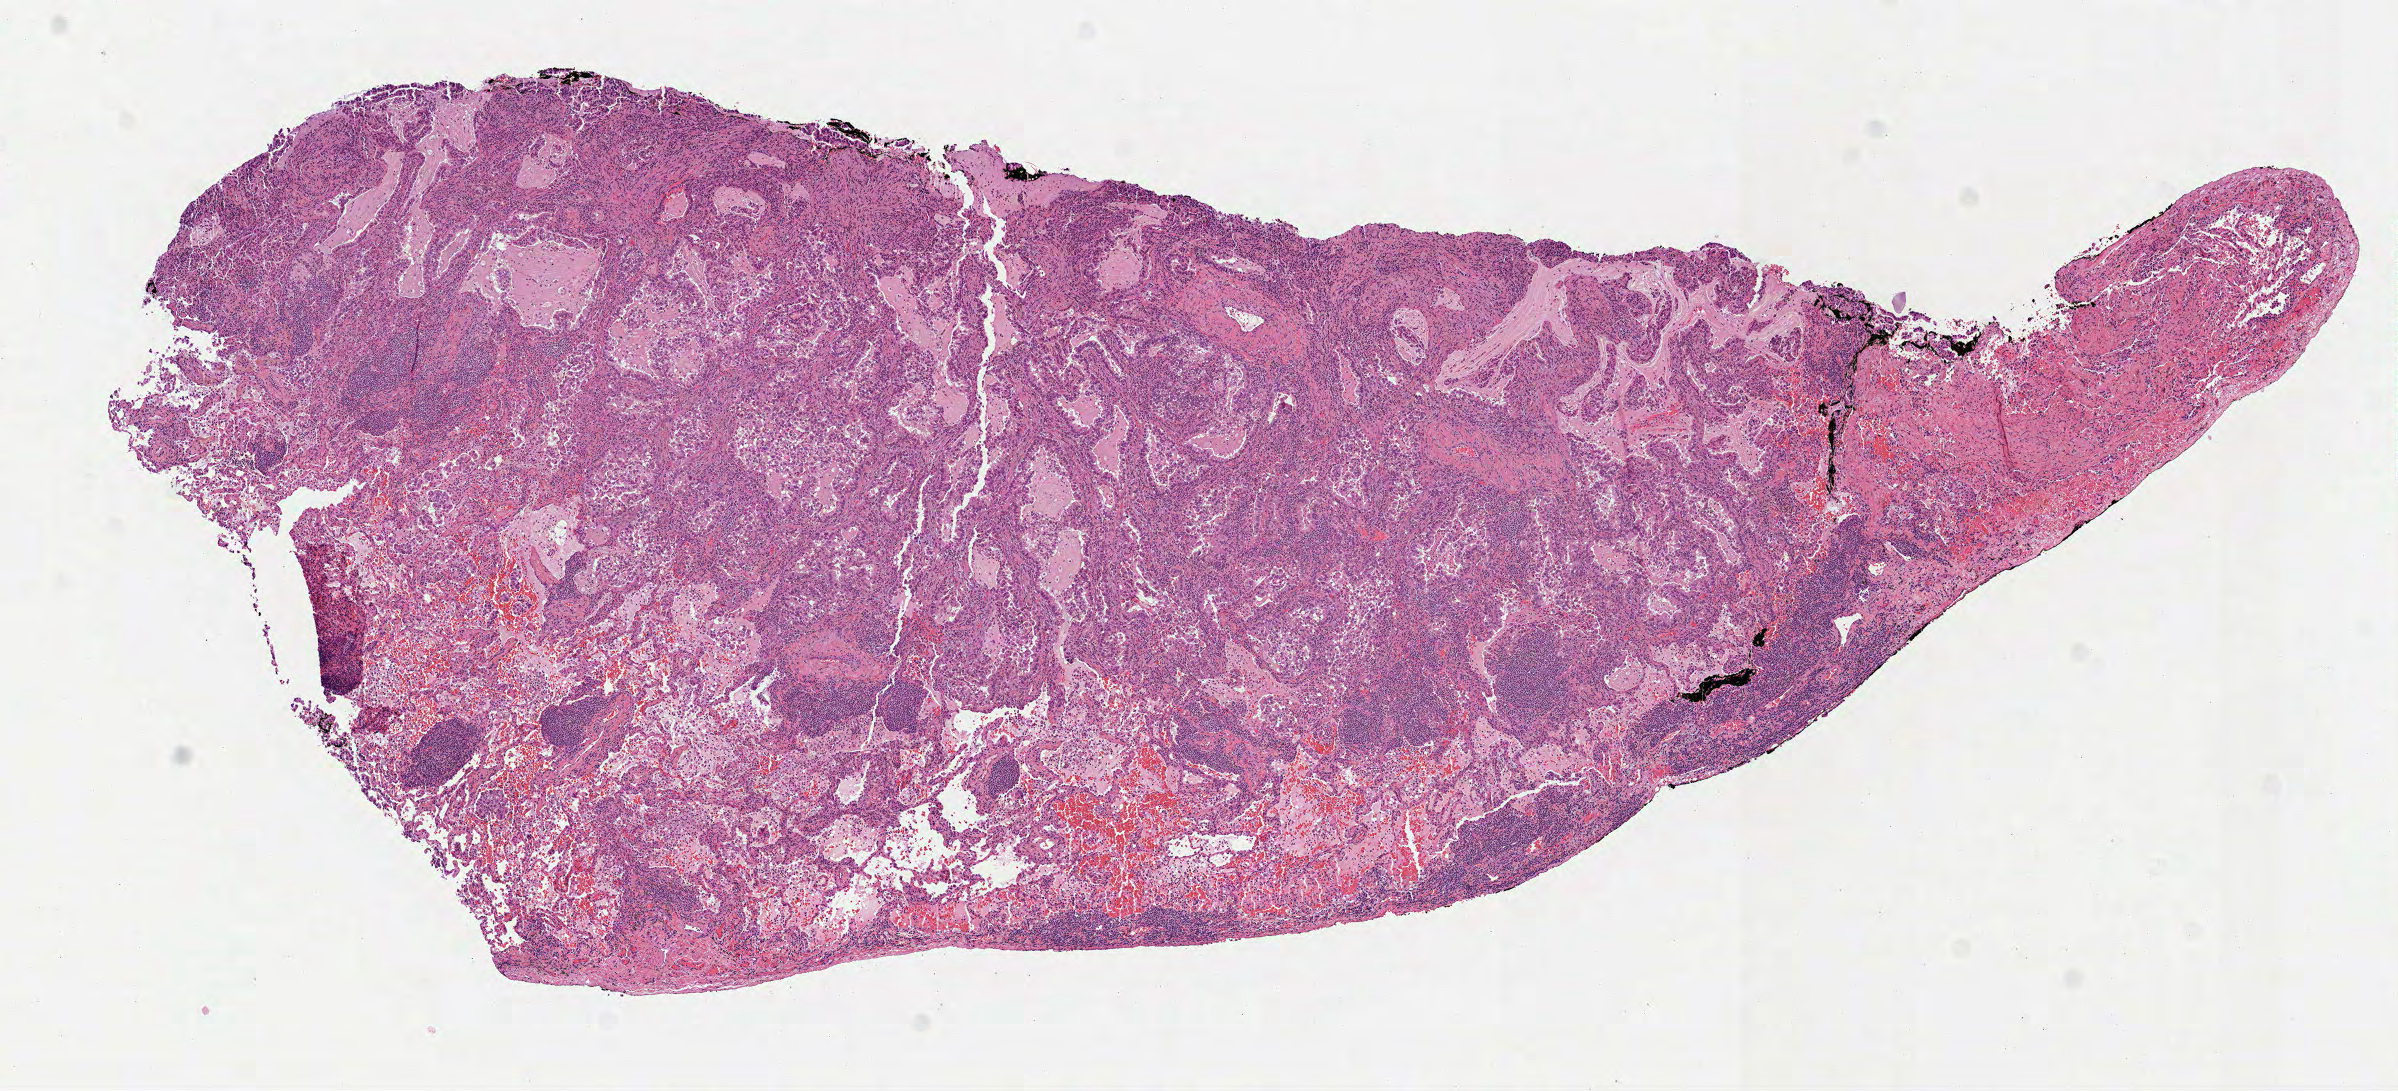
H&E-stained whole-slide image — a low-resolution overview of the entire scanned area, about 9.7 x 4.4 mm (slide scanned at 40x), FFPE section, sample: primary tumour, lung. Female, age 69 years at initial diagnosis.
Diagnosis: Adenocarcinoma, NOS (lower lobe, lung). Laterality: right. AJCC pathologic stage: IA. TNM: T1b N0 M0.